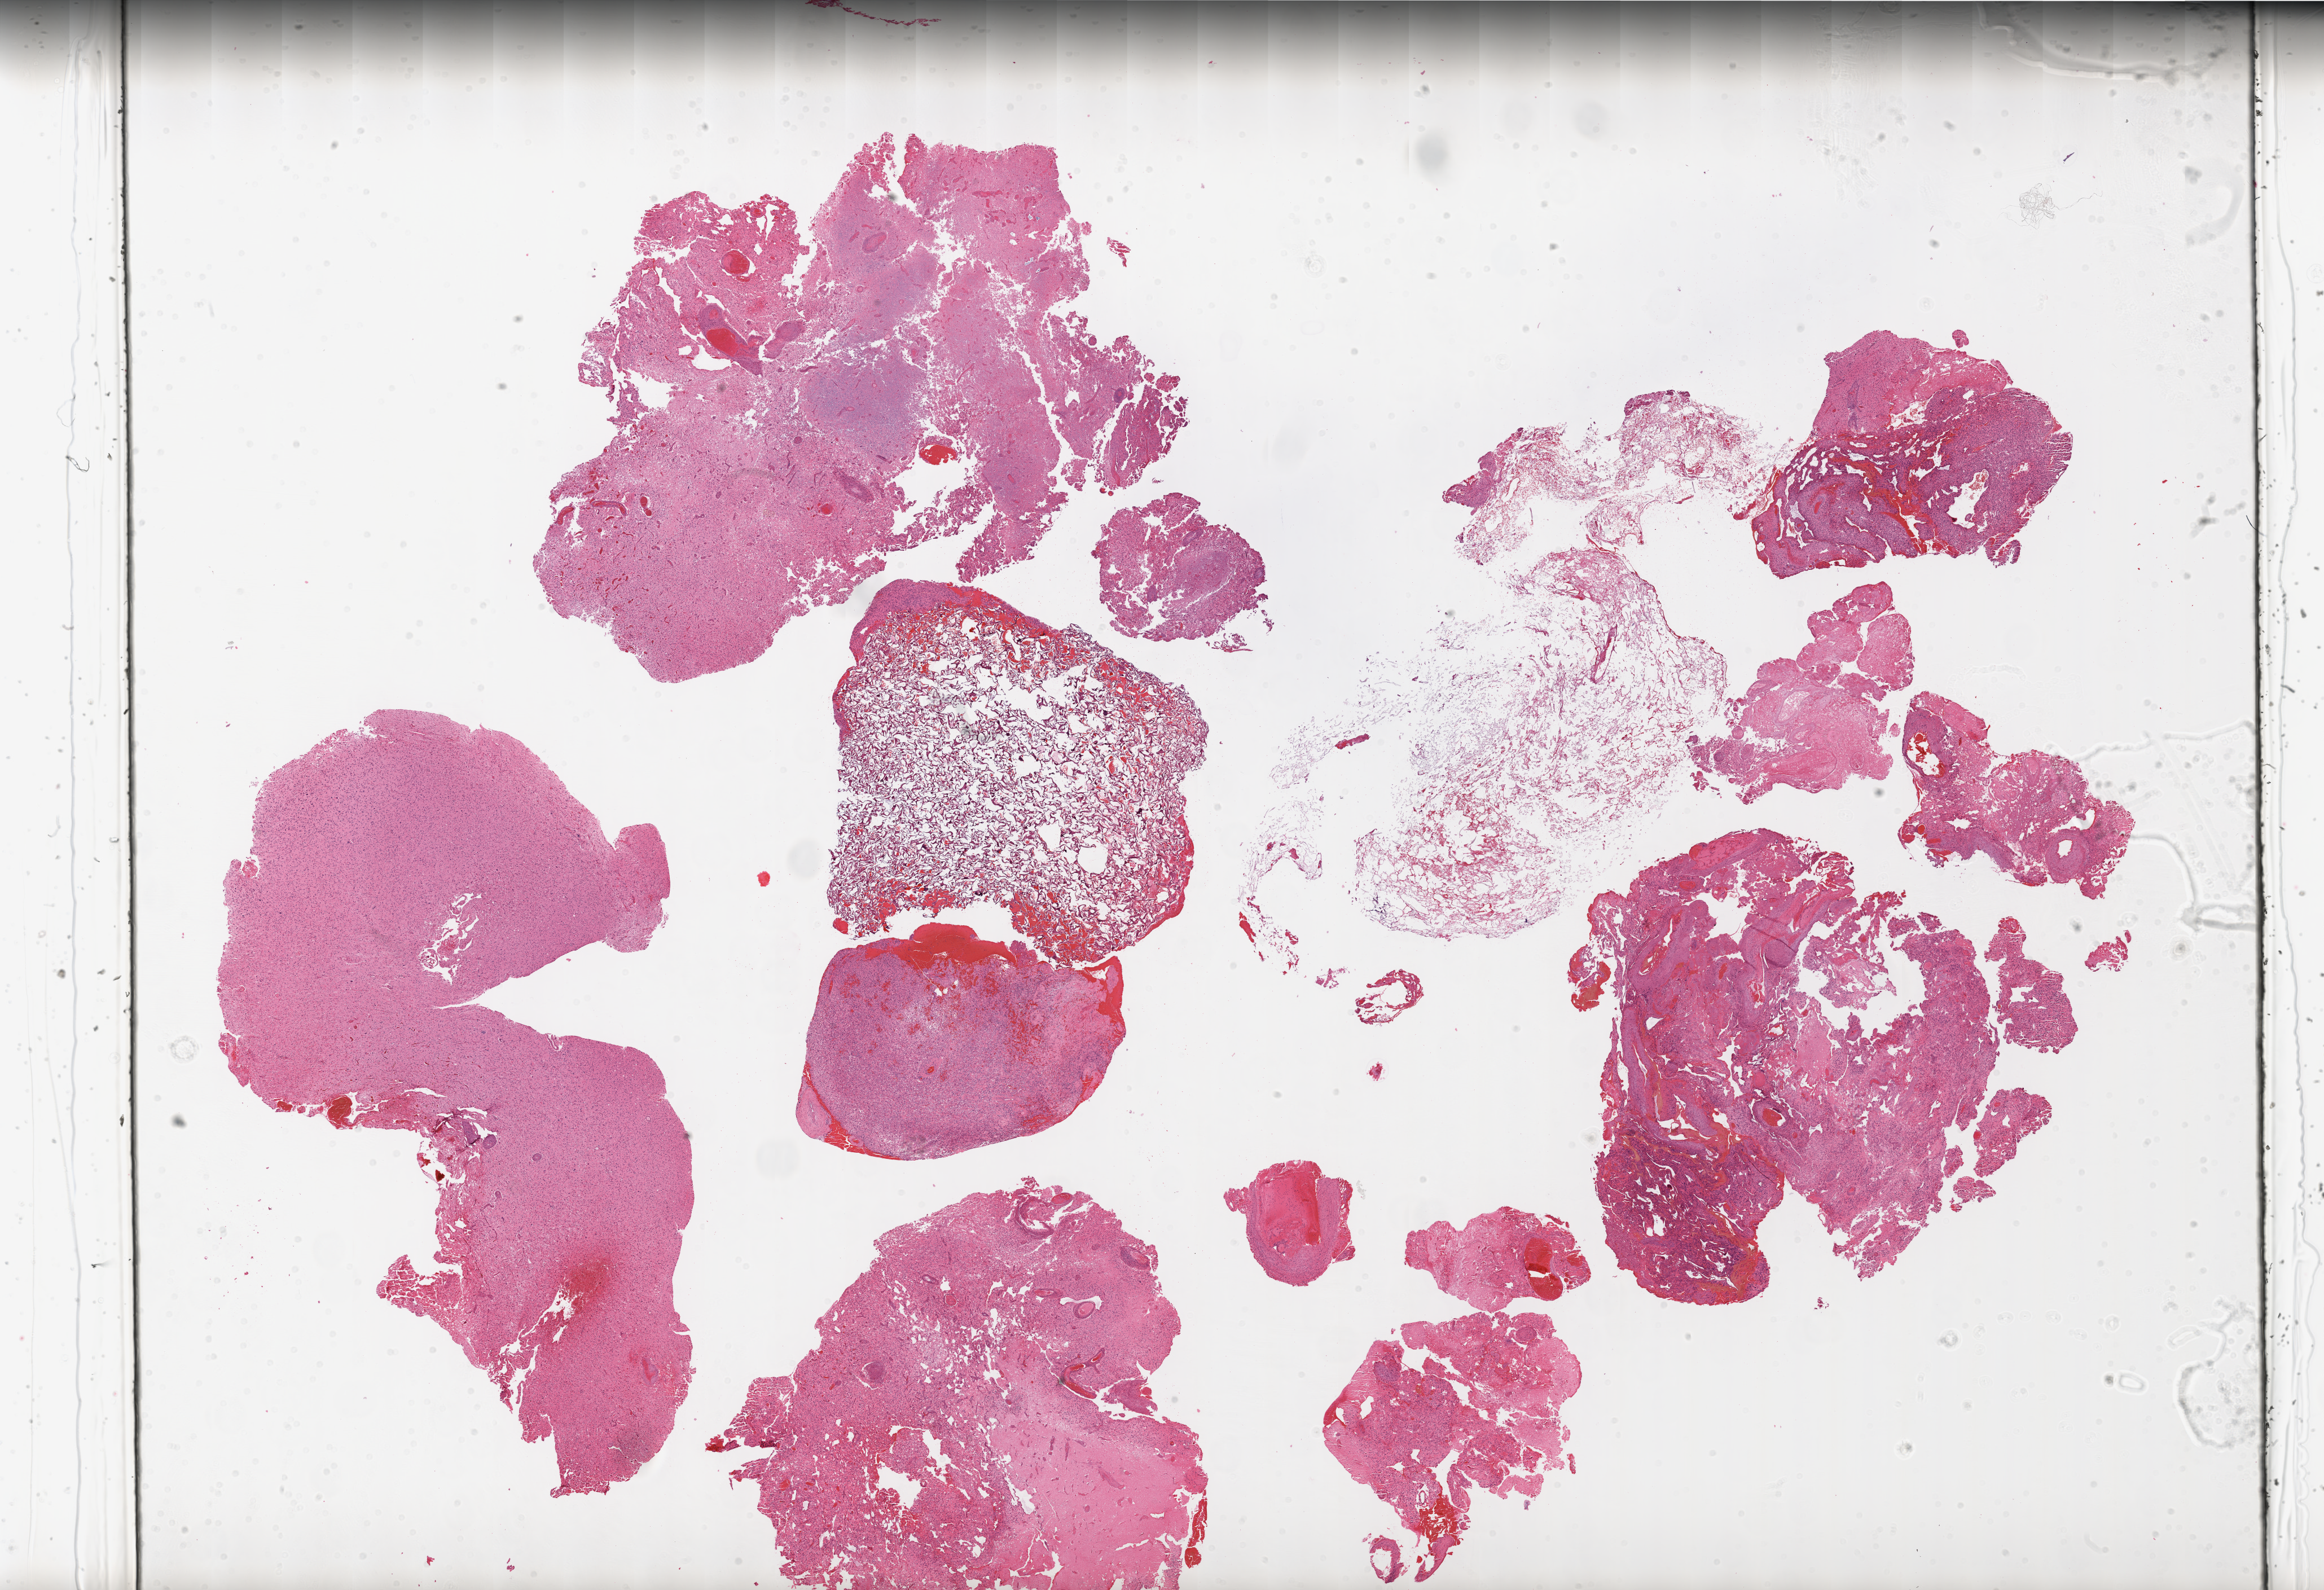
Hematoxylin and eosin (H&E) stained whole-slide image, whole scanned area (about 33.0 x 22.6 mm) shown as a low-resolution overview. FFPE section. Sample: primary tumour, brain. Patient: male, age at initial diagnosis 76 years.
Histologic diagnosis: Glioblastoma.